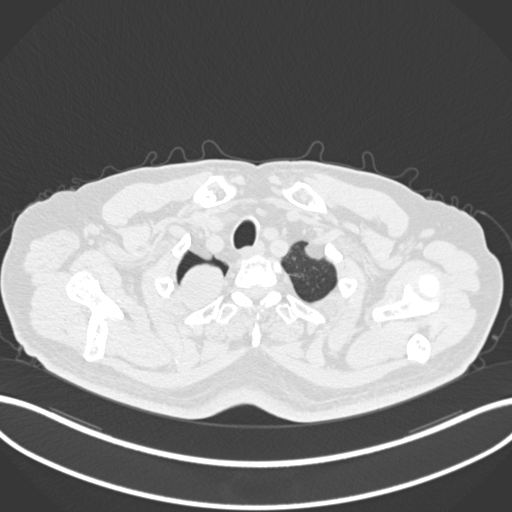
Chest CT, one axial slice. Slice 199 of 218 in the series (ordered by position). Reconstruction kernel B30f. Lung window (W 1500 / L -600 HU). 1 mm slice thickness. 512 × 512 image matrix, field of view 400 × 400 mm. Male patient, age 68 years. Case-level facts recorded for this patient, not image findings: clinical TNM (as recorded): T2a N0 M0.
Annotated regions visible in this slice (rectangle marked by the reading radiologist):
- lung tumour (recorded histology: adenocarcinoma): box from (x=179, y=259) to (x=229, y=306) px